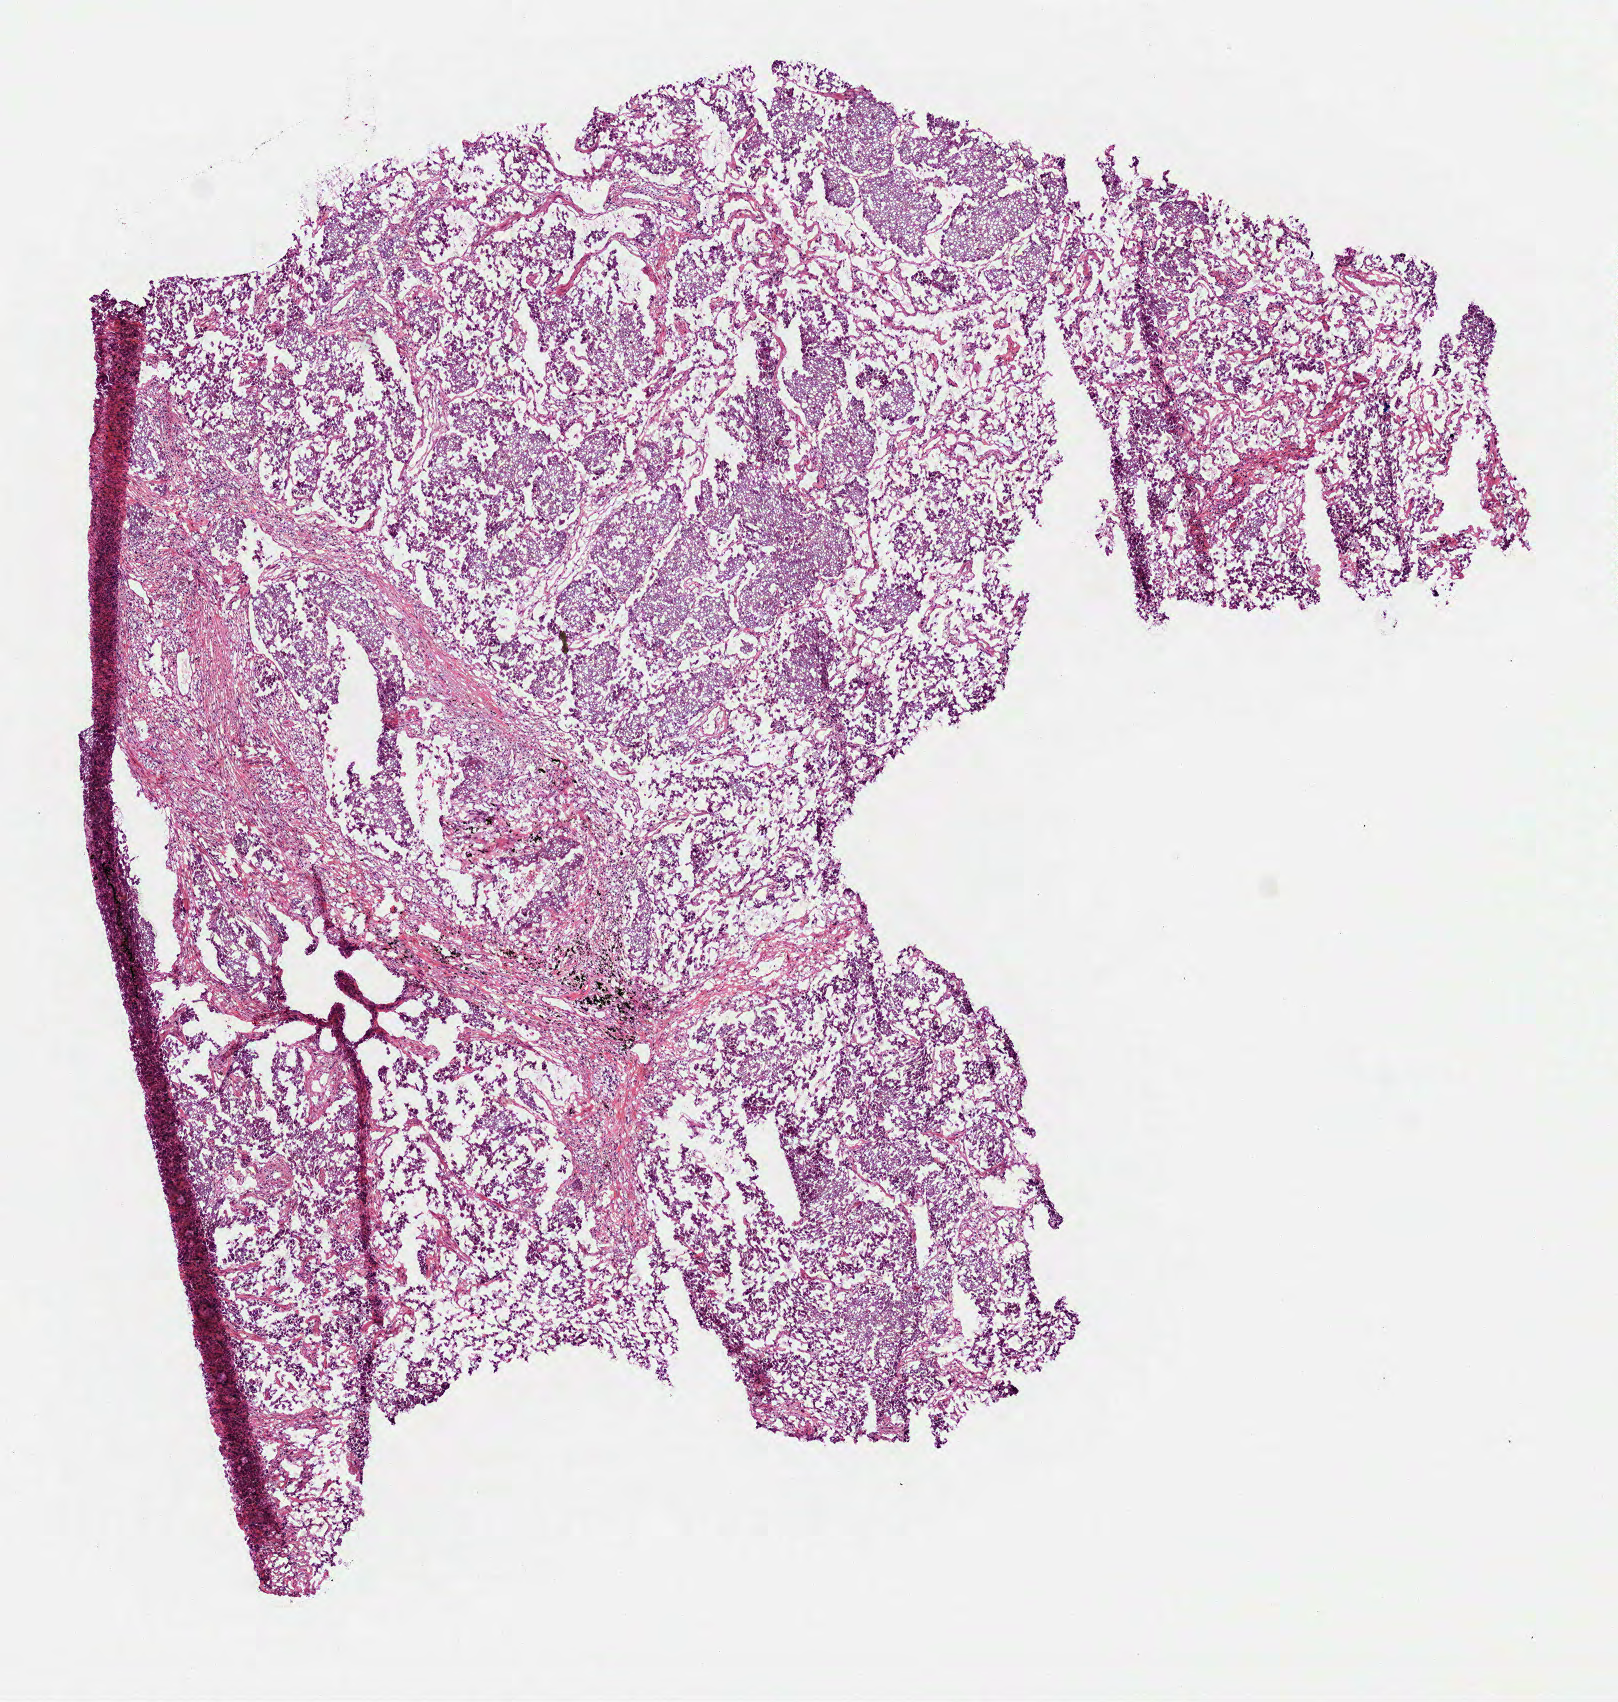
H&E-stained whole-slide image — whole scanned area (about 6.5 x 6.9 mm, slide scanned at 40x) shown as a low-resolution overview; frozen section from the top of the tissue portion; sample: primary tumour, lung. Male, age 72 years at initial diagnosis. Slide review estimates, as recorded: tumour cells 85%, tumour nuclei 80%, normal cells 5%, stromal cells 10%, necrosis 0%.
AJCC pathologic stage: IIIA (6th edition). Pathologic diagnosis: Adenocarcinoma, NOS (upper lobe, lung).